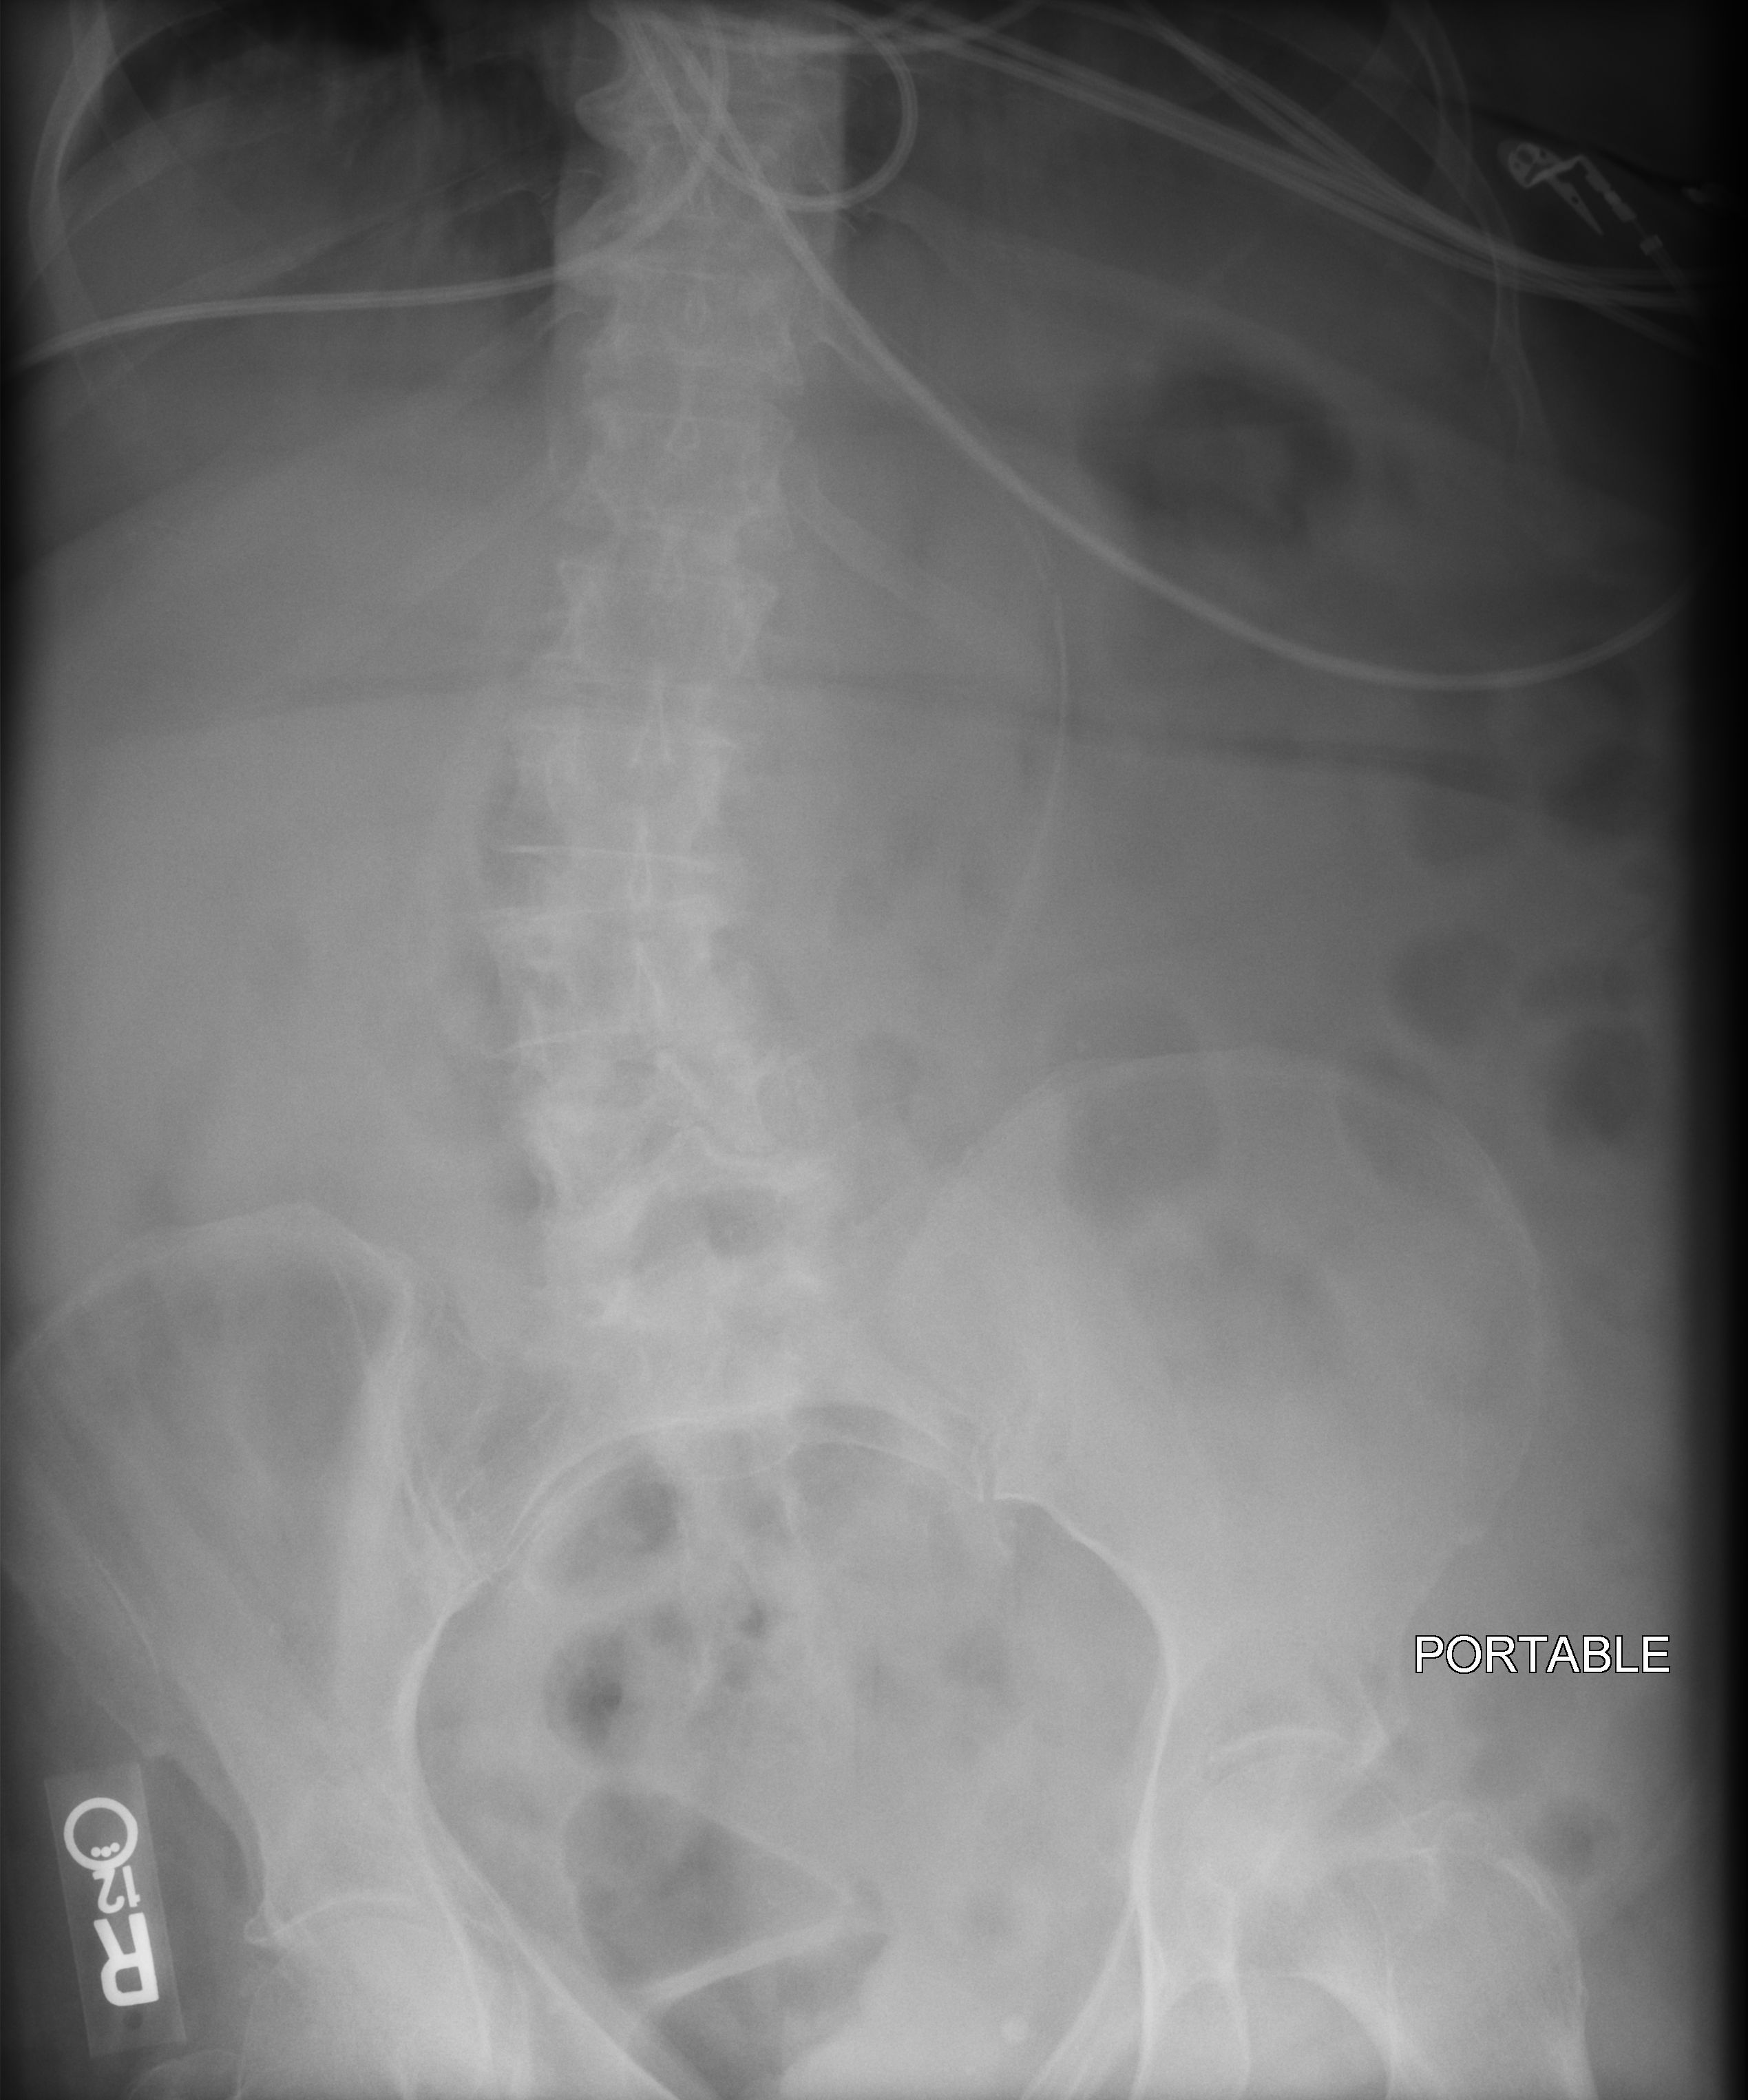
Abdomen X-ray (portable). Patient hospitalised with COVID-19; female, aged 75–90 years.
From the hospital-stay record, not from the radiograph (when in the stay this image was taken is not recorded): smoking status (admission record): former.